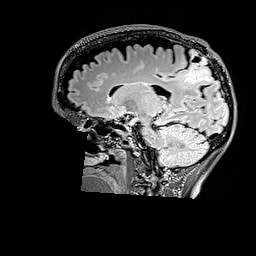
Brain MRI from a brain-tumour surgery series, one sagittal slice; position 104 of 176 along the scan axis; T2 FLAIR; 1 mm slice thickness; 256 × 256 image matrix, field of view 256 × 256 mm. Case-level facts recorded for this patient, not image findings: histopathology: Astrocytoma; WHO grade: 3; IDH mutation: yes; tumour location: Right Parietal.
Annotated regions visible in this slice (manually delineated by an expert):
- tumour: bounding box <181,49,212,83> (left, top, right, bottom; pixels)
- tumour: <186,57,214,83>